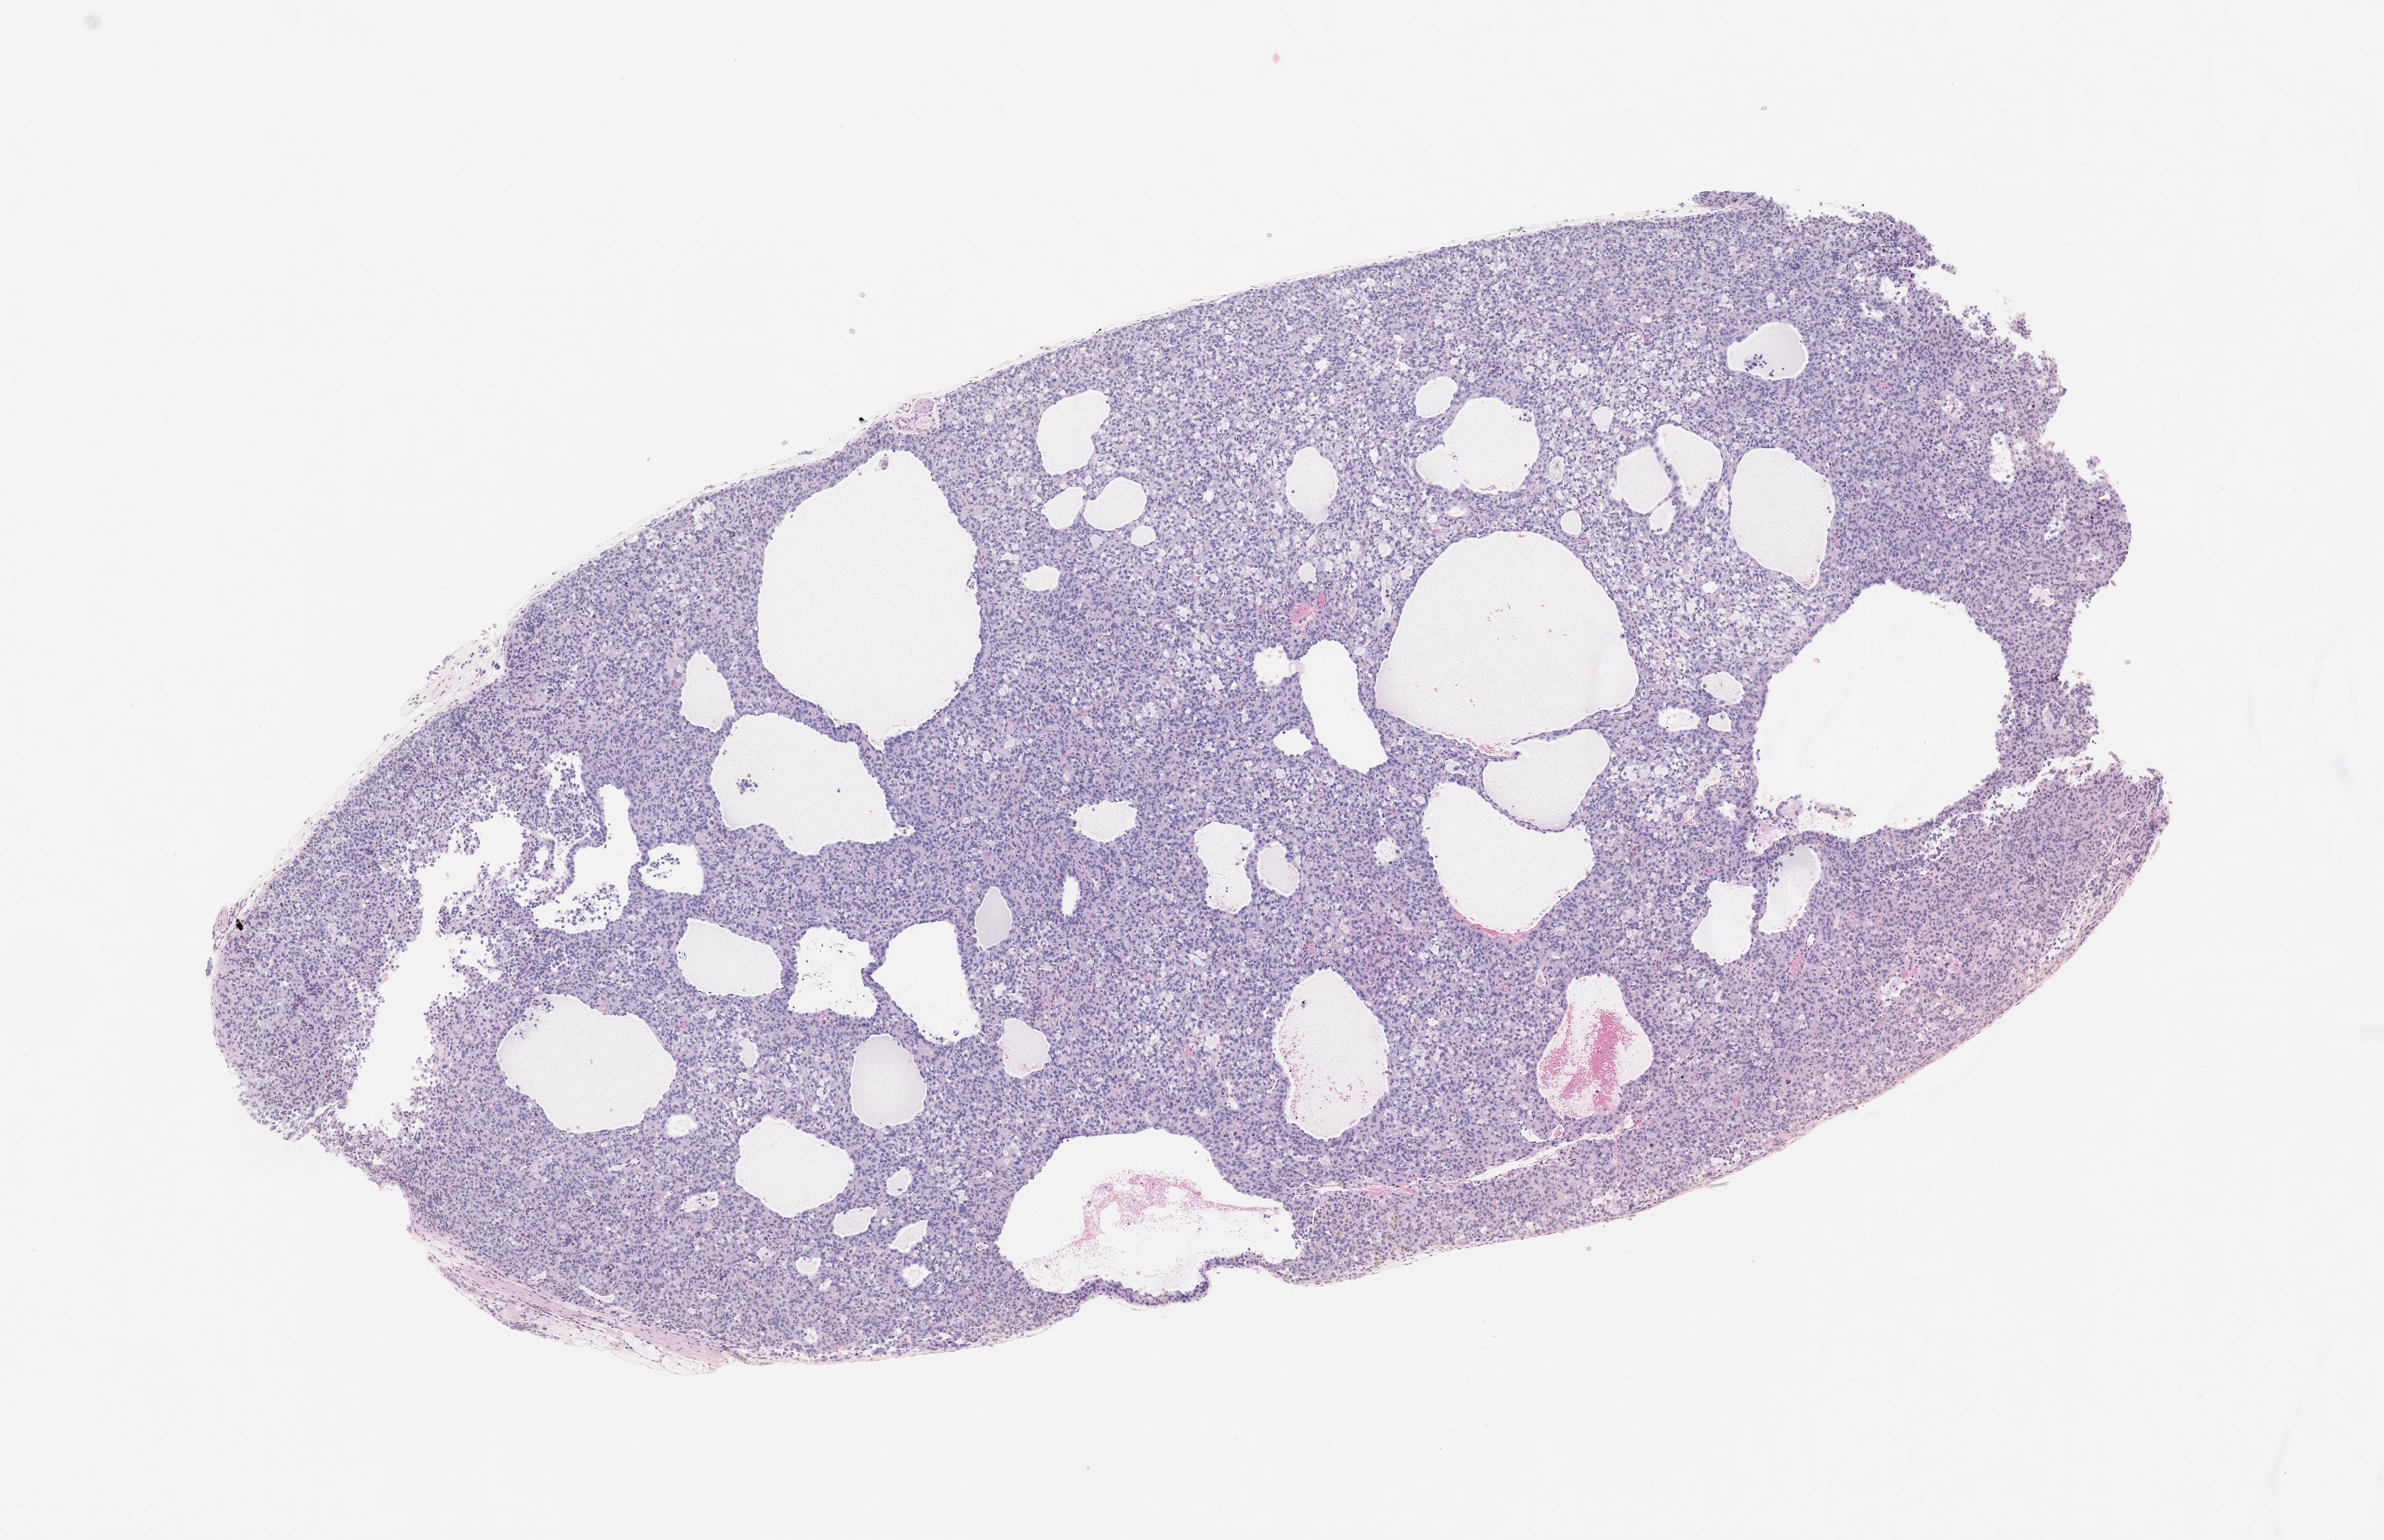
Whole-slide image, H&E: patient-derived xenograft (human tumor grown in a mouse), passage 1 — low-resolution overview of the scanned area, about 8.0 x 5.2 mm, FFPE section, originating tumor site category: uterus.
Originating patient diagnosis: Leiomyosarcoma.